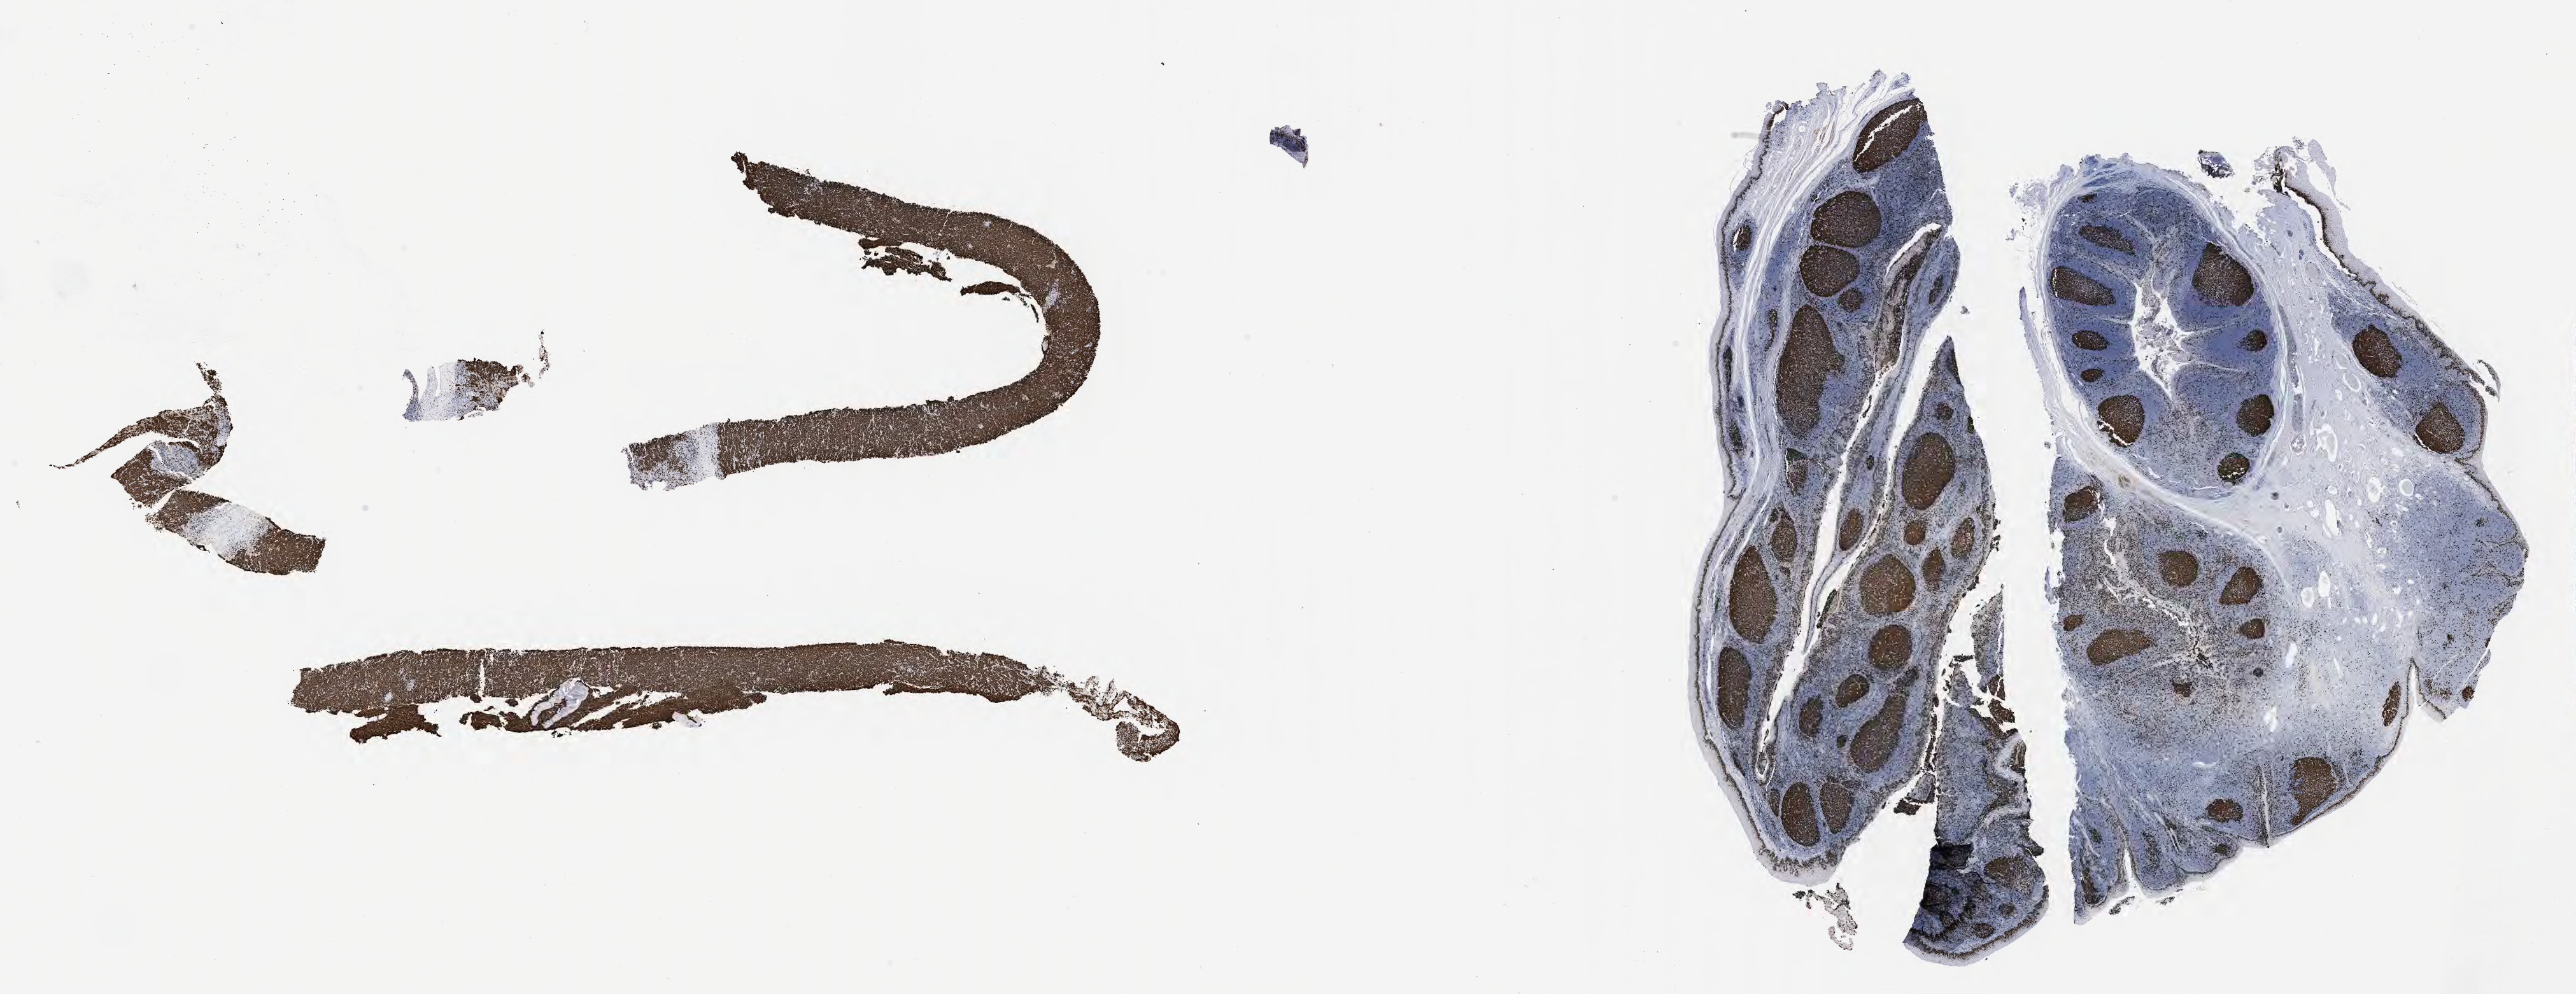
Immunohistochemistry (IHC) whole-slide image stained for Ki-67, whole scanned area (about 32.7 x 12.6 mm) shown as a low-resolution overview. Tumor tissue. Patient male; age 55 years.
* histologic diagnosis: Burkitt lymphoma, NOS